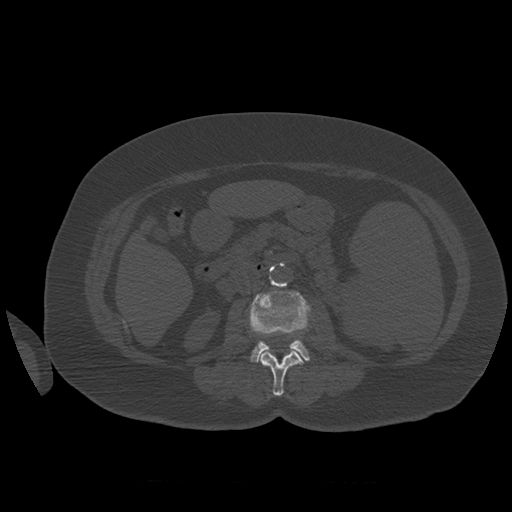
CT including the spine, one axial slice; slice 242 of 399 in the series (ordered by position); 120 kVp; bone window (W 1800 / L 400 HU); 512 × 512 image matrix, field of view 404 × 404 mm. Patient age 81 years. From the clinical record (not read from this slice): primary cancer: renal; vertebrae with lytic lesions (as recorded): L1.
Annotated regions visible in this slice (semi-automatic segmentation, software-assisted and operator-edited):
- L2 vertebra: bounding box (x1, y1, x2, y2) in pixels: (260, 348, 304, 396)
- L3 vertebra: (249, 289, 311, 363)